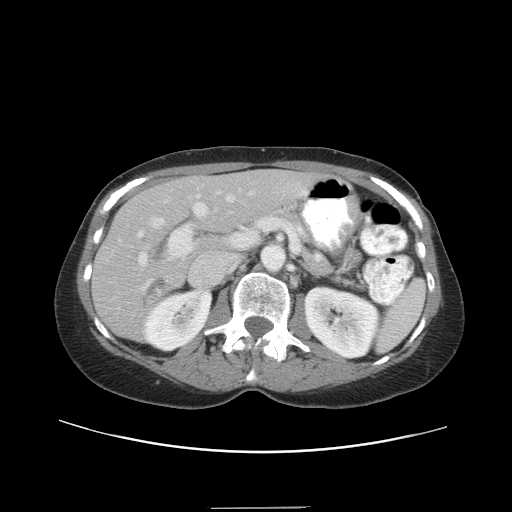
Contrast-enhanced abdominal CT, one axial slice. Position 21 of 38 along the scan axis. Reconstruction kernel STANDARD. Intravenous contrast given. Soft-tissue window (W 400 / L 40 HU). 5 mm slice thickness. 512 × 512 image matrix, field of view 388 × 388 mm. Female patient, age 64 years. Case-level facts recorded for this patient, not image findings: diagnosis: colorectal cancer liver metastases, imaged before liver resection; multiple liver metastases: no; largest metastasis: 3.8 cm; chemotherapy before resection: yes.
Structures marked on this image (expert manual segmentation):
- hepatic veins: bounding box (x1, y1, x2, y2) in pixels: (133, 191, 253, 316)
- liver: (93, 169, 312, 339)
- planned liver remnant (the part of the liver to remain after resection): (137, 169, 312, 233)
- portal vein (with intrahepatic branches): (131, 191, 244, 265)